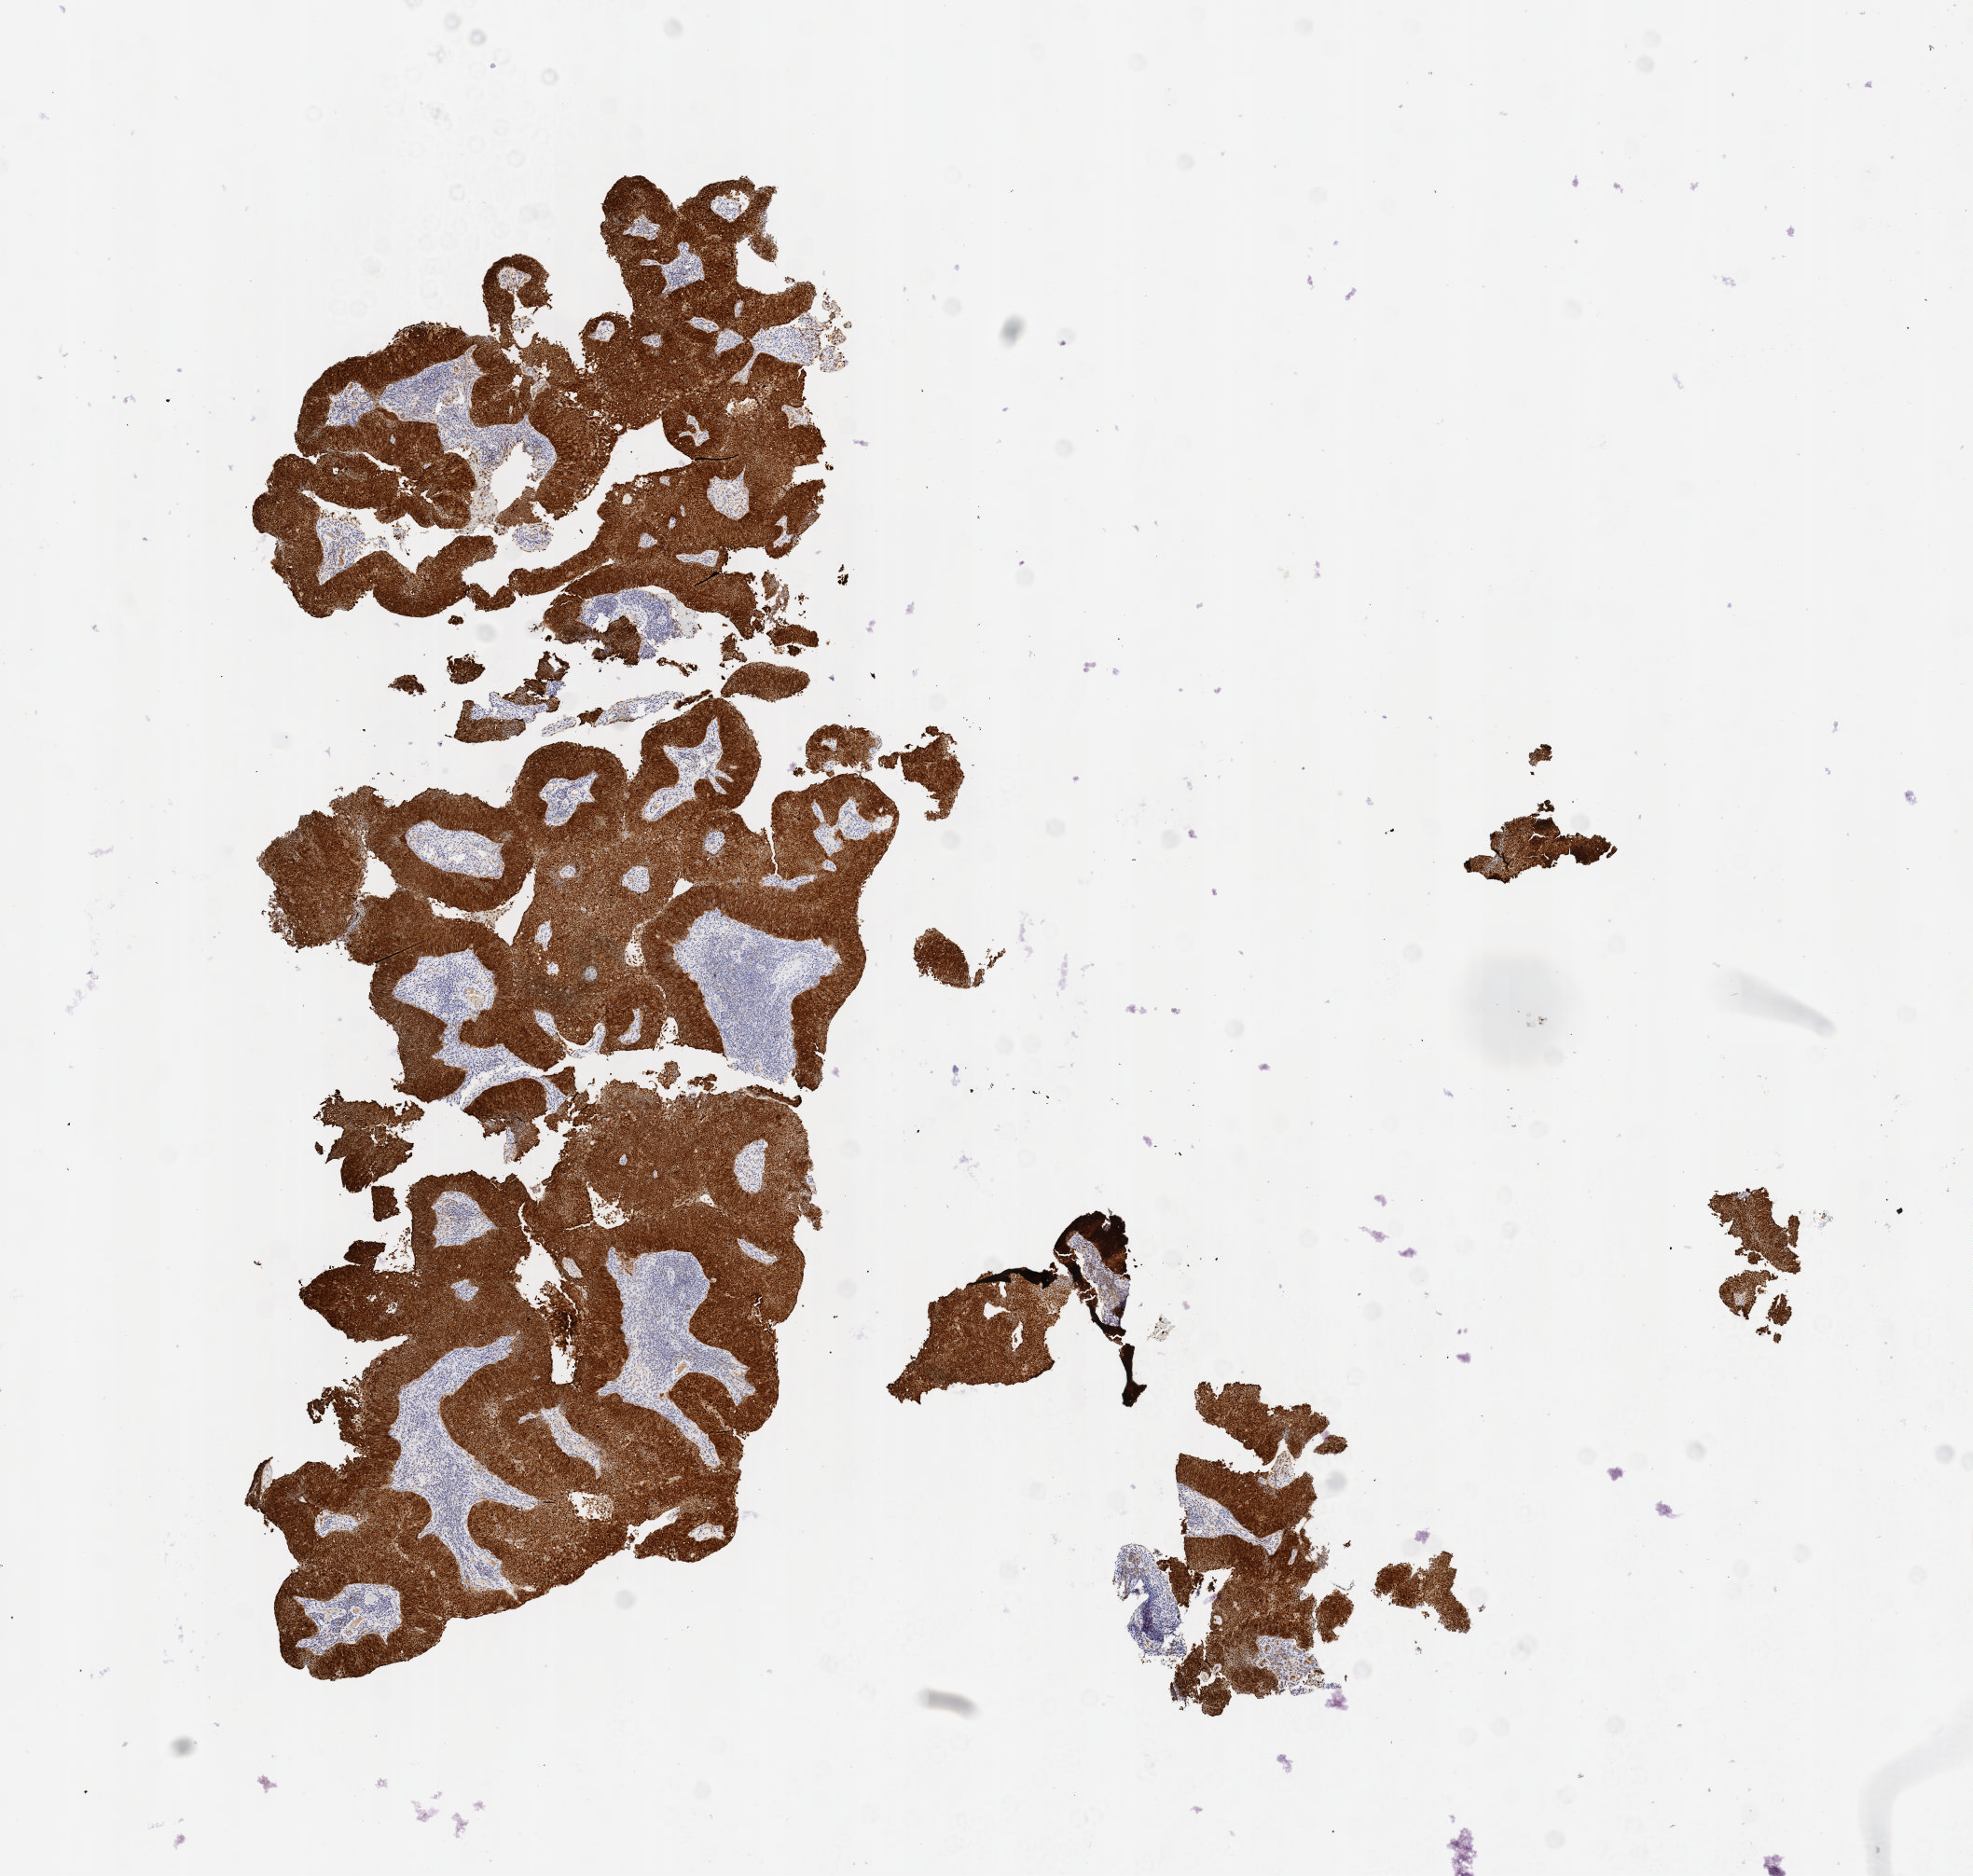
Immunohistochemistry (IHC) whole-slide image stained for p16 (p16INK4a), whole scanned area (about 8.6 x 8.1 mm) shown as a low-resolution overview, specimen: tumor tissue, site: cervix. Patient: female, age 42 years.
- histologic diagnosis: Squamous cell carcinoma, large cell, nonkeratinizing, NOS